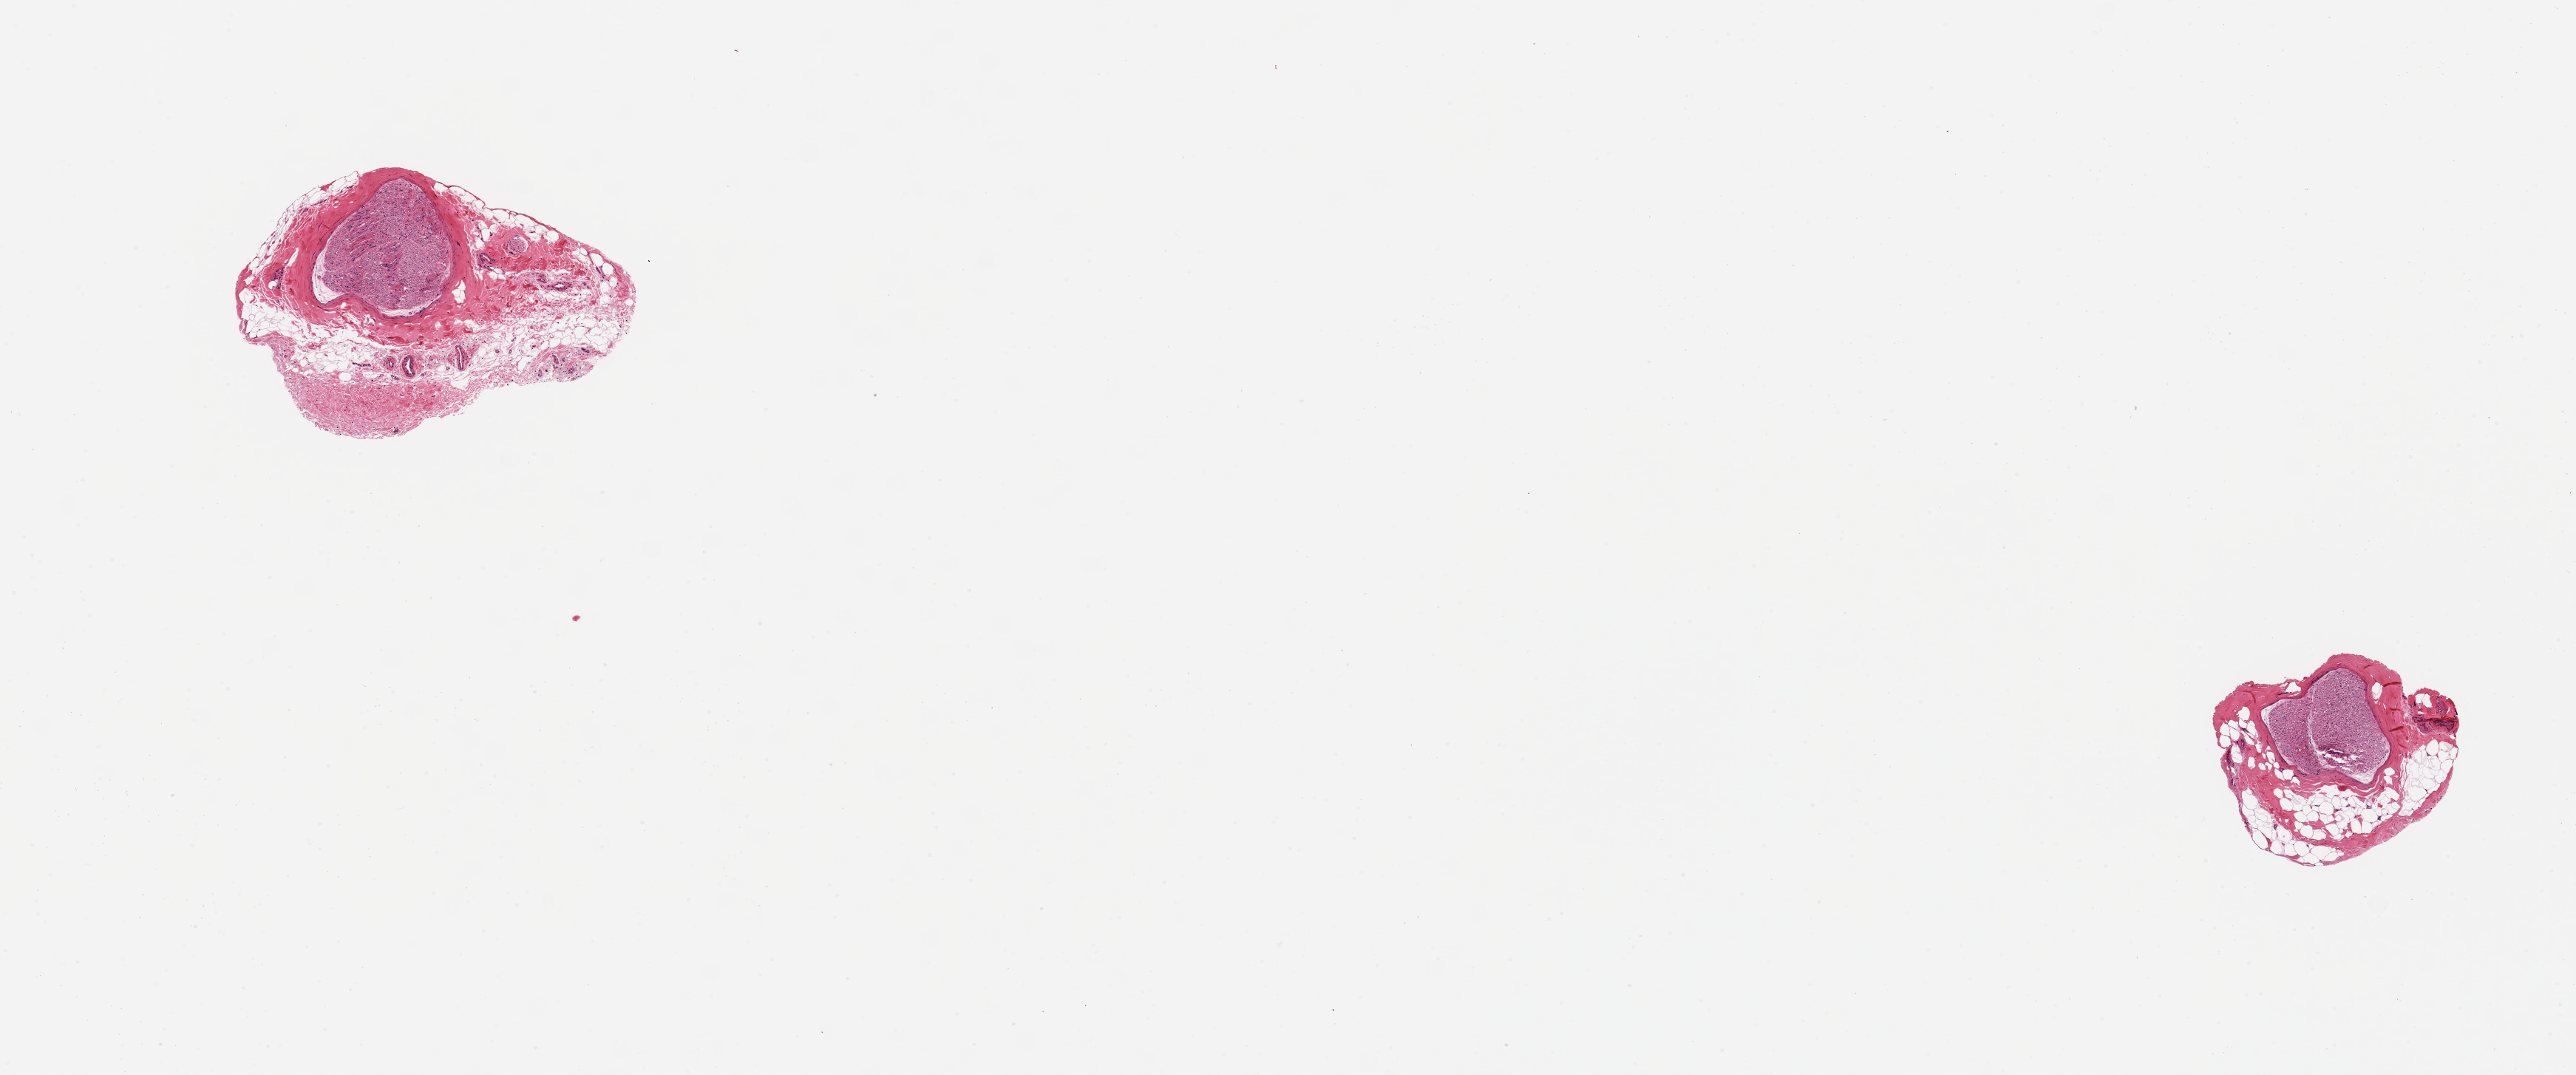
Digitized haematoxylin and eosin-stained section — shown as a low-resolution overview of the whole scanned area (about 13.8 x 5.7 mm, slide scanned at 20x); PAXgene-fixed paraffin-embedded (PFPE) section; target tissue: tibial nerve; donor tissue sample. Donor sex: male.
Review note (as recorded): 2 pieces, central 0.5mm nerve, surrounded by rind of 0.5-1mm fat/fibrous tissue.